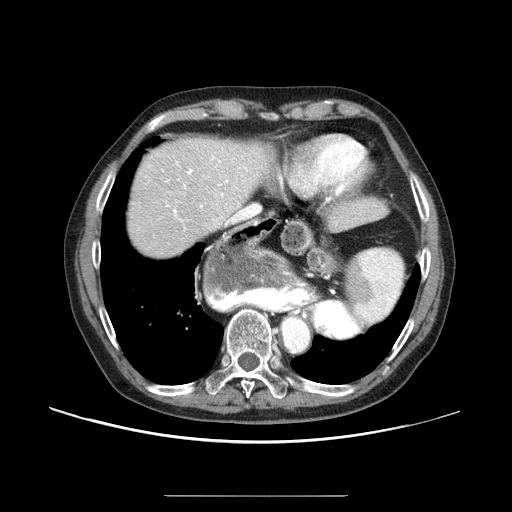
Contrast-enhanced abdominal CT (liver protocol), one axial slice. Position 75 of 91 along the scan axis. Reconstruction kernel STANDARD. 100 kVp. One of 2 acquisitions stored at this slice position. Soft-tissue window (W 400 / L 40 HU). 2.5 mm slice thickness. 512 × 512 image matrix, field of view 400 × 400 mm. From the clinical record (not read from this slice): diagnosis: hepatocellular carcinoma (patient treated with transarterial chemoembolisation; whether this scan precedes or follows treatment is not stated here); TNM stage (as recorded): Stage-I; Child-Pugh class: A.
Outlined on this slice (semi-automatically segmented with operator editing):
- abdominal aorta: bounding box (x1, y1, x2, y2) in pixels: (282, 318, 308, 351)
- liver parenchyma outside the tumour (the mass and vessels are separate outlines, so this box may not span the whole liver): (128, 138, 272, 256)
- liver vessels: (166, 157, 247, 225)